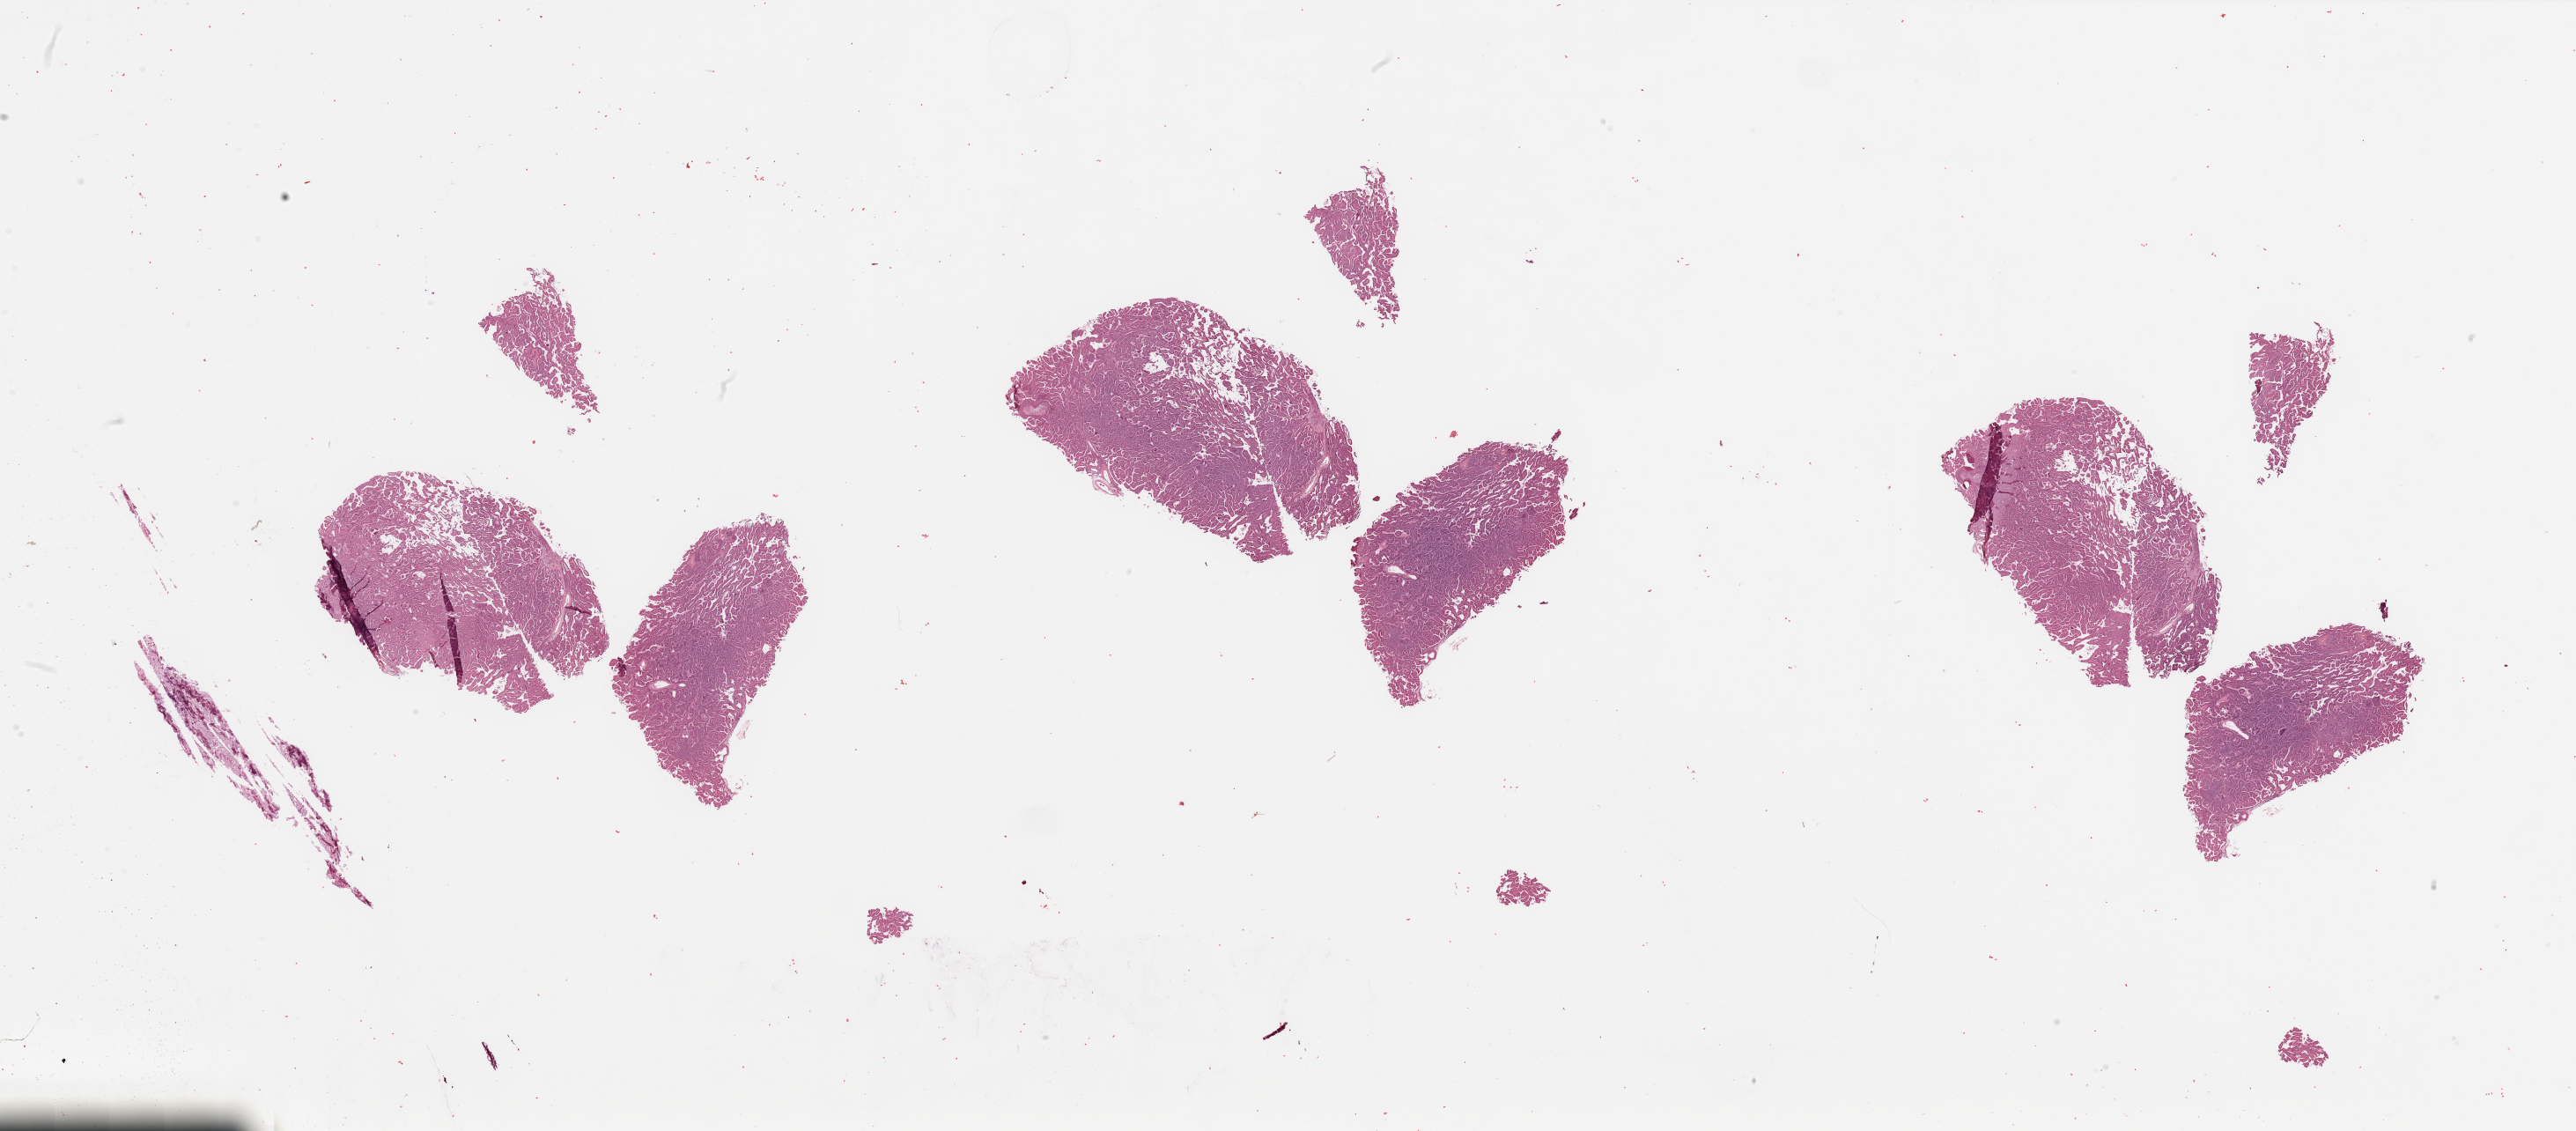
Digitized Hematoxylin and eosin (H&E) stained tissue section (whole slide), a low-resolution overview of the entire scanned area, about 46.3 x 20.3 mm (slide scanned at 20x), tumour tissue sample, lung. Patient: female, age 66 years. Histologic grade: G1 (well differentiated).
AJCC pathologic stage: IIB. Primary tumour site (as recorded): right lower lobe. Histologic diagnosis: Adenocarcinoma, NOS.